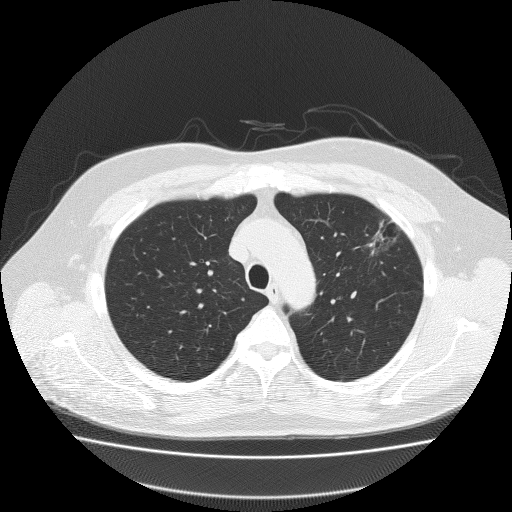
Chest CT (low-dose screening protocol), one axial image. Baseline annual screen. Lung window (W 1500 / L -600 HU). Slice 49 of 204 in the series. 512 × 512 image matrix, field of view 410 × 410 mm. Male, age 62 years at enrolment.
- Expert reader's lesion annotation, bounding box [x1, y1, x2, y2] px = [350, 212, 418, 266].
- Reader record for this screening exam (exam-level; its link to the box is not recorded): non-calcified nodule or mass ≥4 mm, left upper lobe, 18 × 8 mm, spiculated (stellate) margins, soft tissue attenuation.
- Lung cancer was diagnosed 49 days after this screen: bronchiolo-alveolar adenocarcinoma, NOS, left upper lobe, well differentiated (G1), stage IA (AJCC 6th edition), 25 mm at pathology.